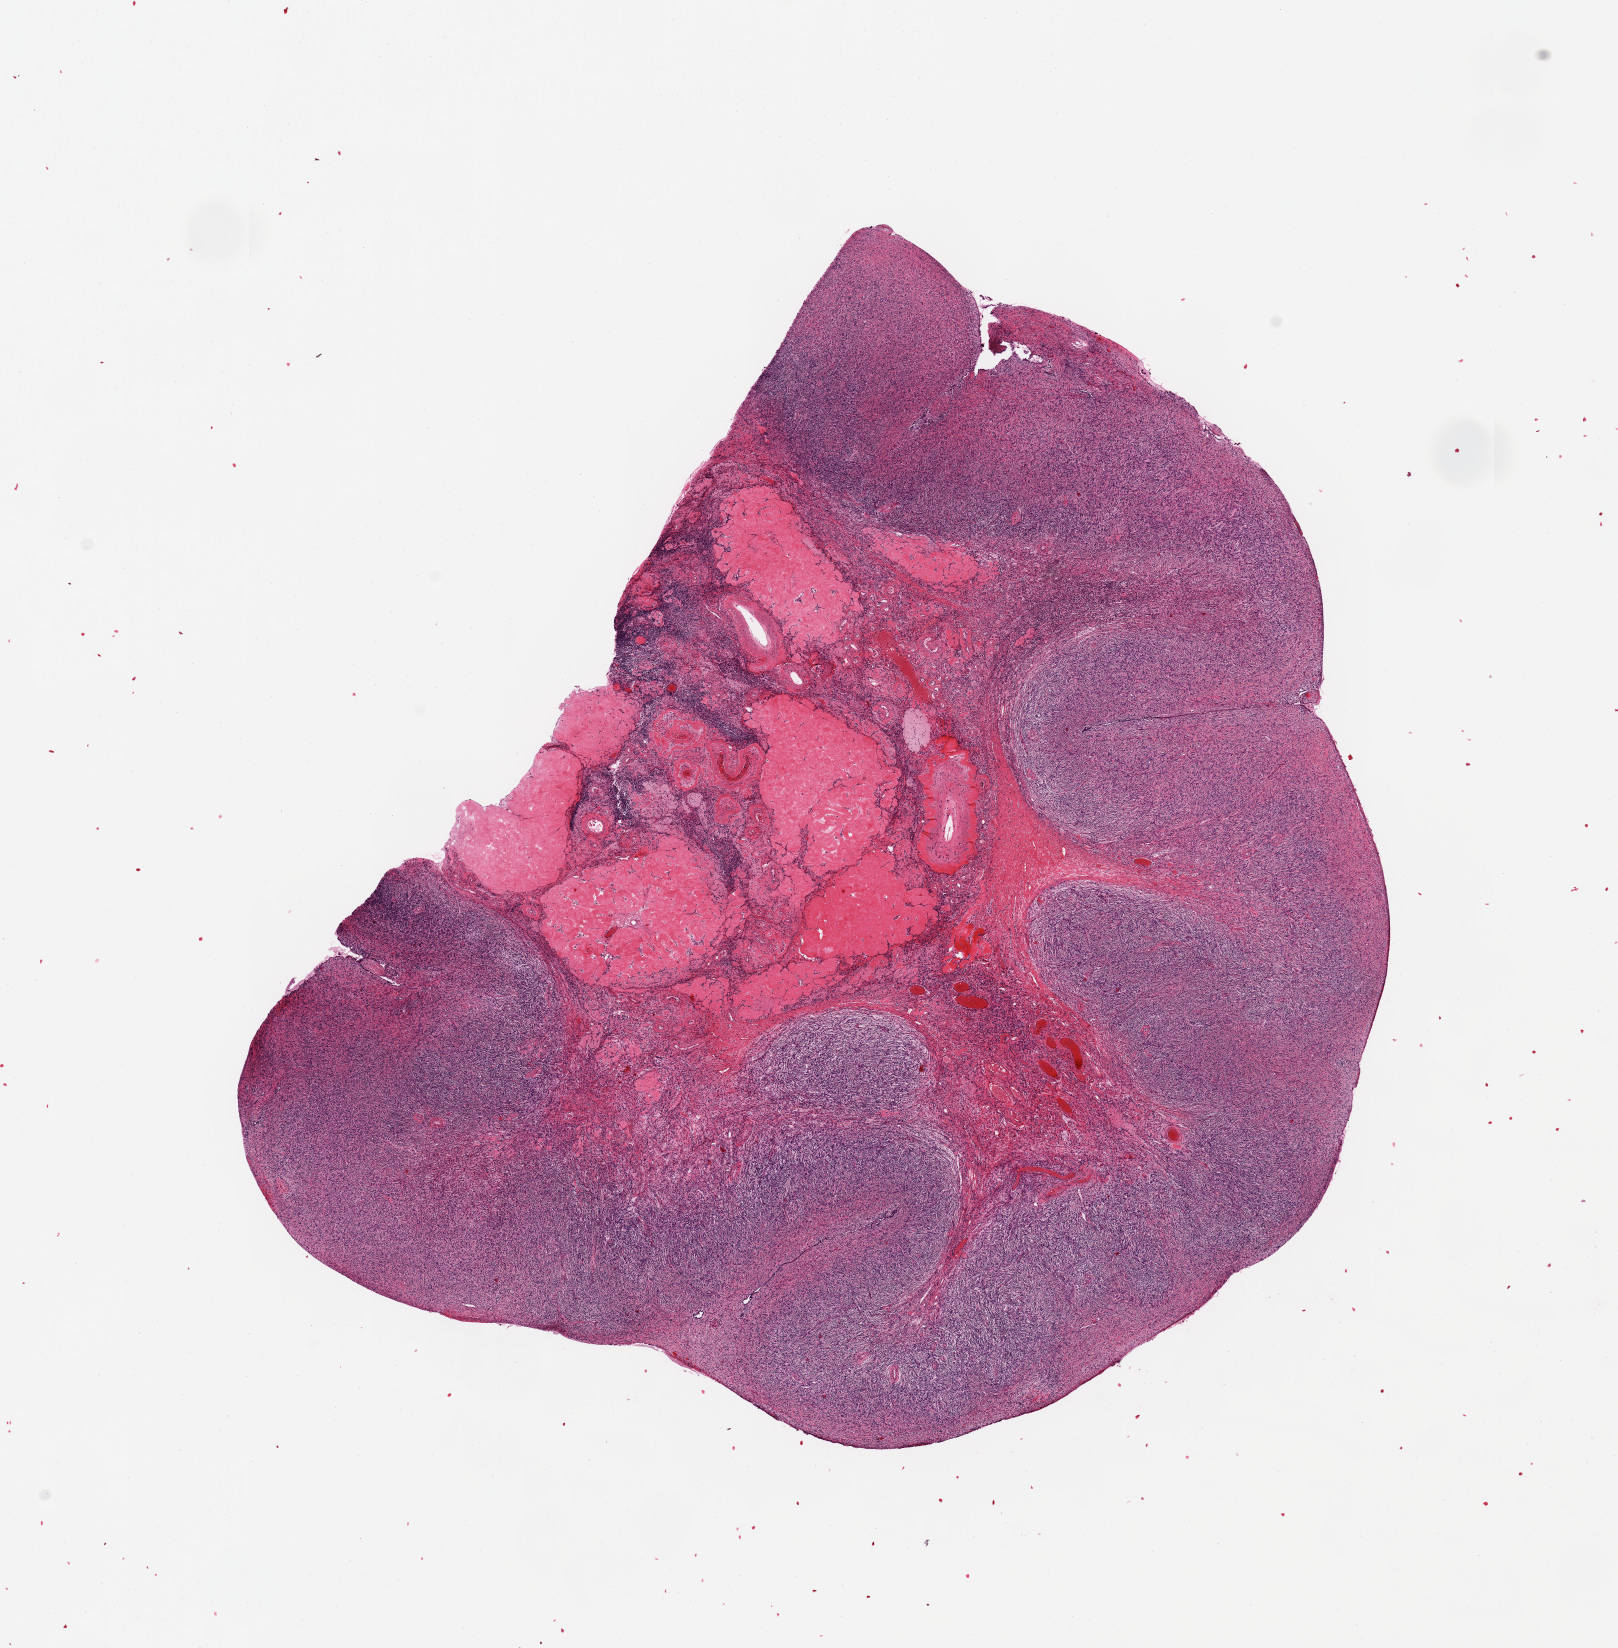
Digitized haematoxylin and eosin-stained section, low-resolution overview of the scanned area, about 12.8 x 13.0 mm (slide scanned at 20x), PAXgene-fixed, paraffin-embedded tissue, target tissue: fallopian tube, tissue donor sample.
Pathologist's review note for this sample: No tube: post menopausal ovary, 9.3x7.1mm.